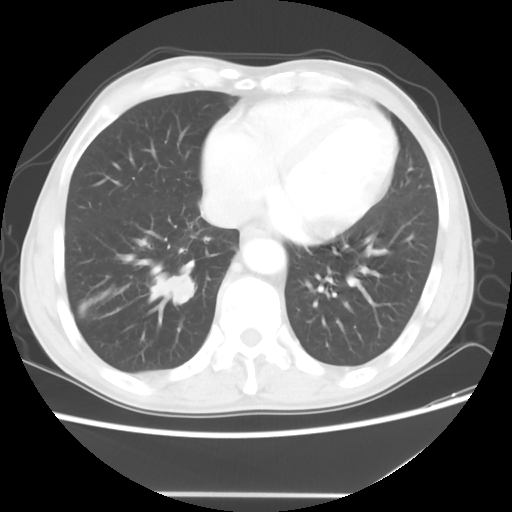
Chest CT, one axial slice. Position 15 of 56 along the scan axis. 120 kVp. Lung window (W 1500 / L -600 HU). 5 mm slice thickness. 512 × 512 image matrix, field of view 344 × 344 mm. Male patient, age 65 years. From the clinical record (not read from this slice): clinical TNM (as recorded): T1c N3 M0; histopathological grade: G3.
Annotated regions visible in this slice (rectangle marked by the reading radiologist):
- lung tumour (recorded histology: small cell carcinoma): bounding box [x1, y1, x2, y2] px = [147, 267, 200, 307]